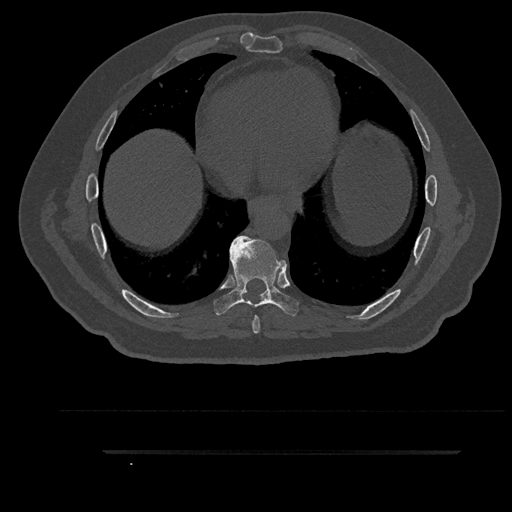
CT including the spine, one axial slice; slice 487 of 797 in the series (ordered by position); reconstruction kernel Br40s/3; bone window (W 1800 / L 400 HU); 0.5 mm slice thickness; 512 × 512 image matrix, field of view 432 × 432 mm. Male patient, age 63 years. Case-level facts recorded for this patient, not image findings: primary cancer: renal; vertebrae with lytic lesions (as recorded): T8.
Annotated regions visible in this slice (semi-automatic segmentation, software-assisted and operator-edited):
- T7 vertebra: bounding box (x1, y1, x2, y2) in pixels: (252, 315, 260, 334)
- T8 vertebra: (214, 235, 299, 316)